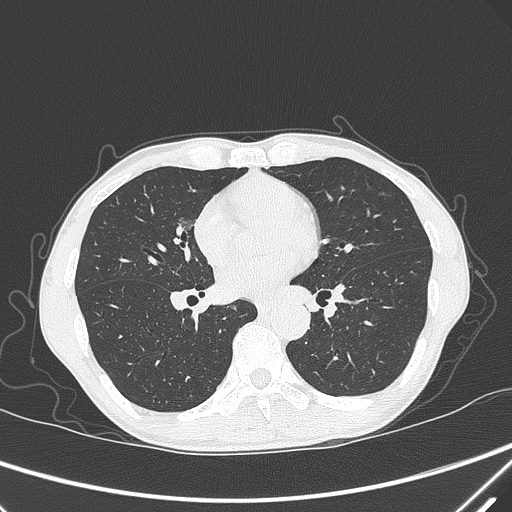
Chest CT, one axial slice. Slice 159 of 339 in the series (ordered by position). Lung window (W 1500 / L -600 HU). 1 mm slice thickness. 512 × 512 image matrix, field of view 350 × 350 mm. Patient: male, 67 years. Case-level facts recorded for this patient, not image findings: clinical TNM (as recorded): T1c N0 M0.
Structures marked on this image (rectangle marked by the reading radiologist):
- lung tumour (recorded histology: adenocarcinoma): box from (x=176, y=209) to (x=193, y=239) px